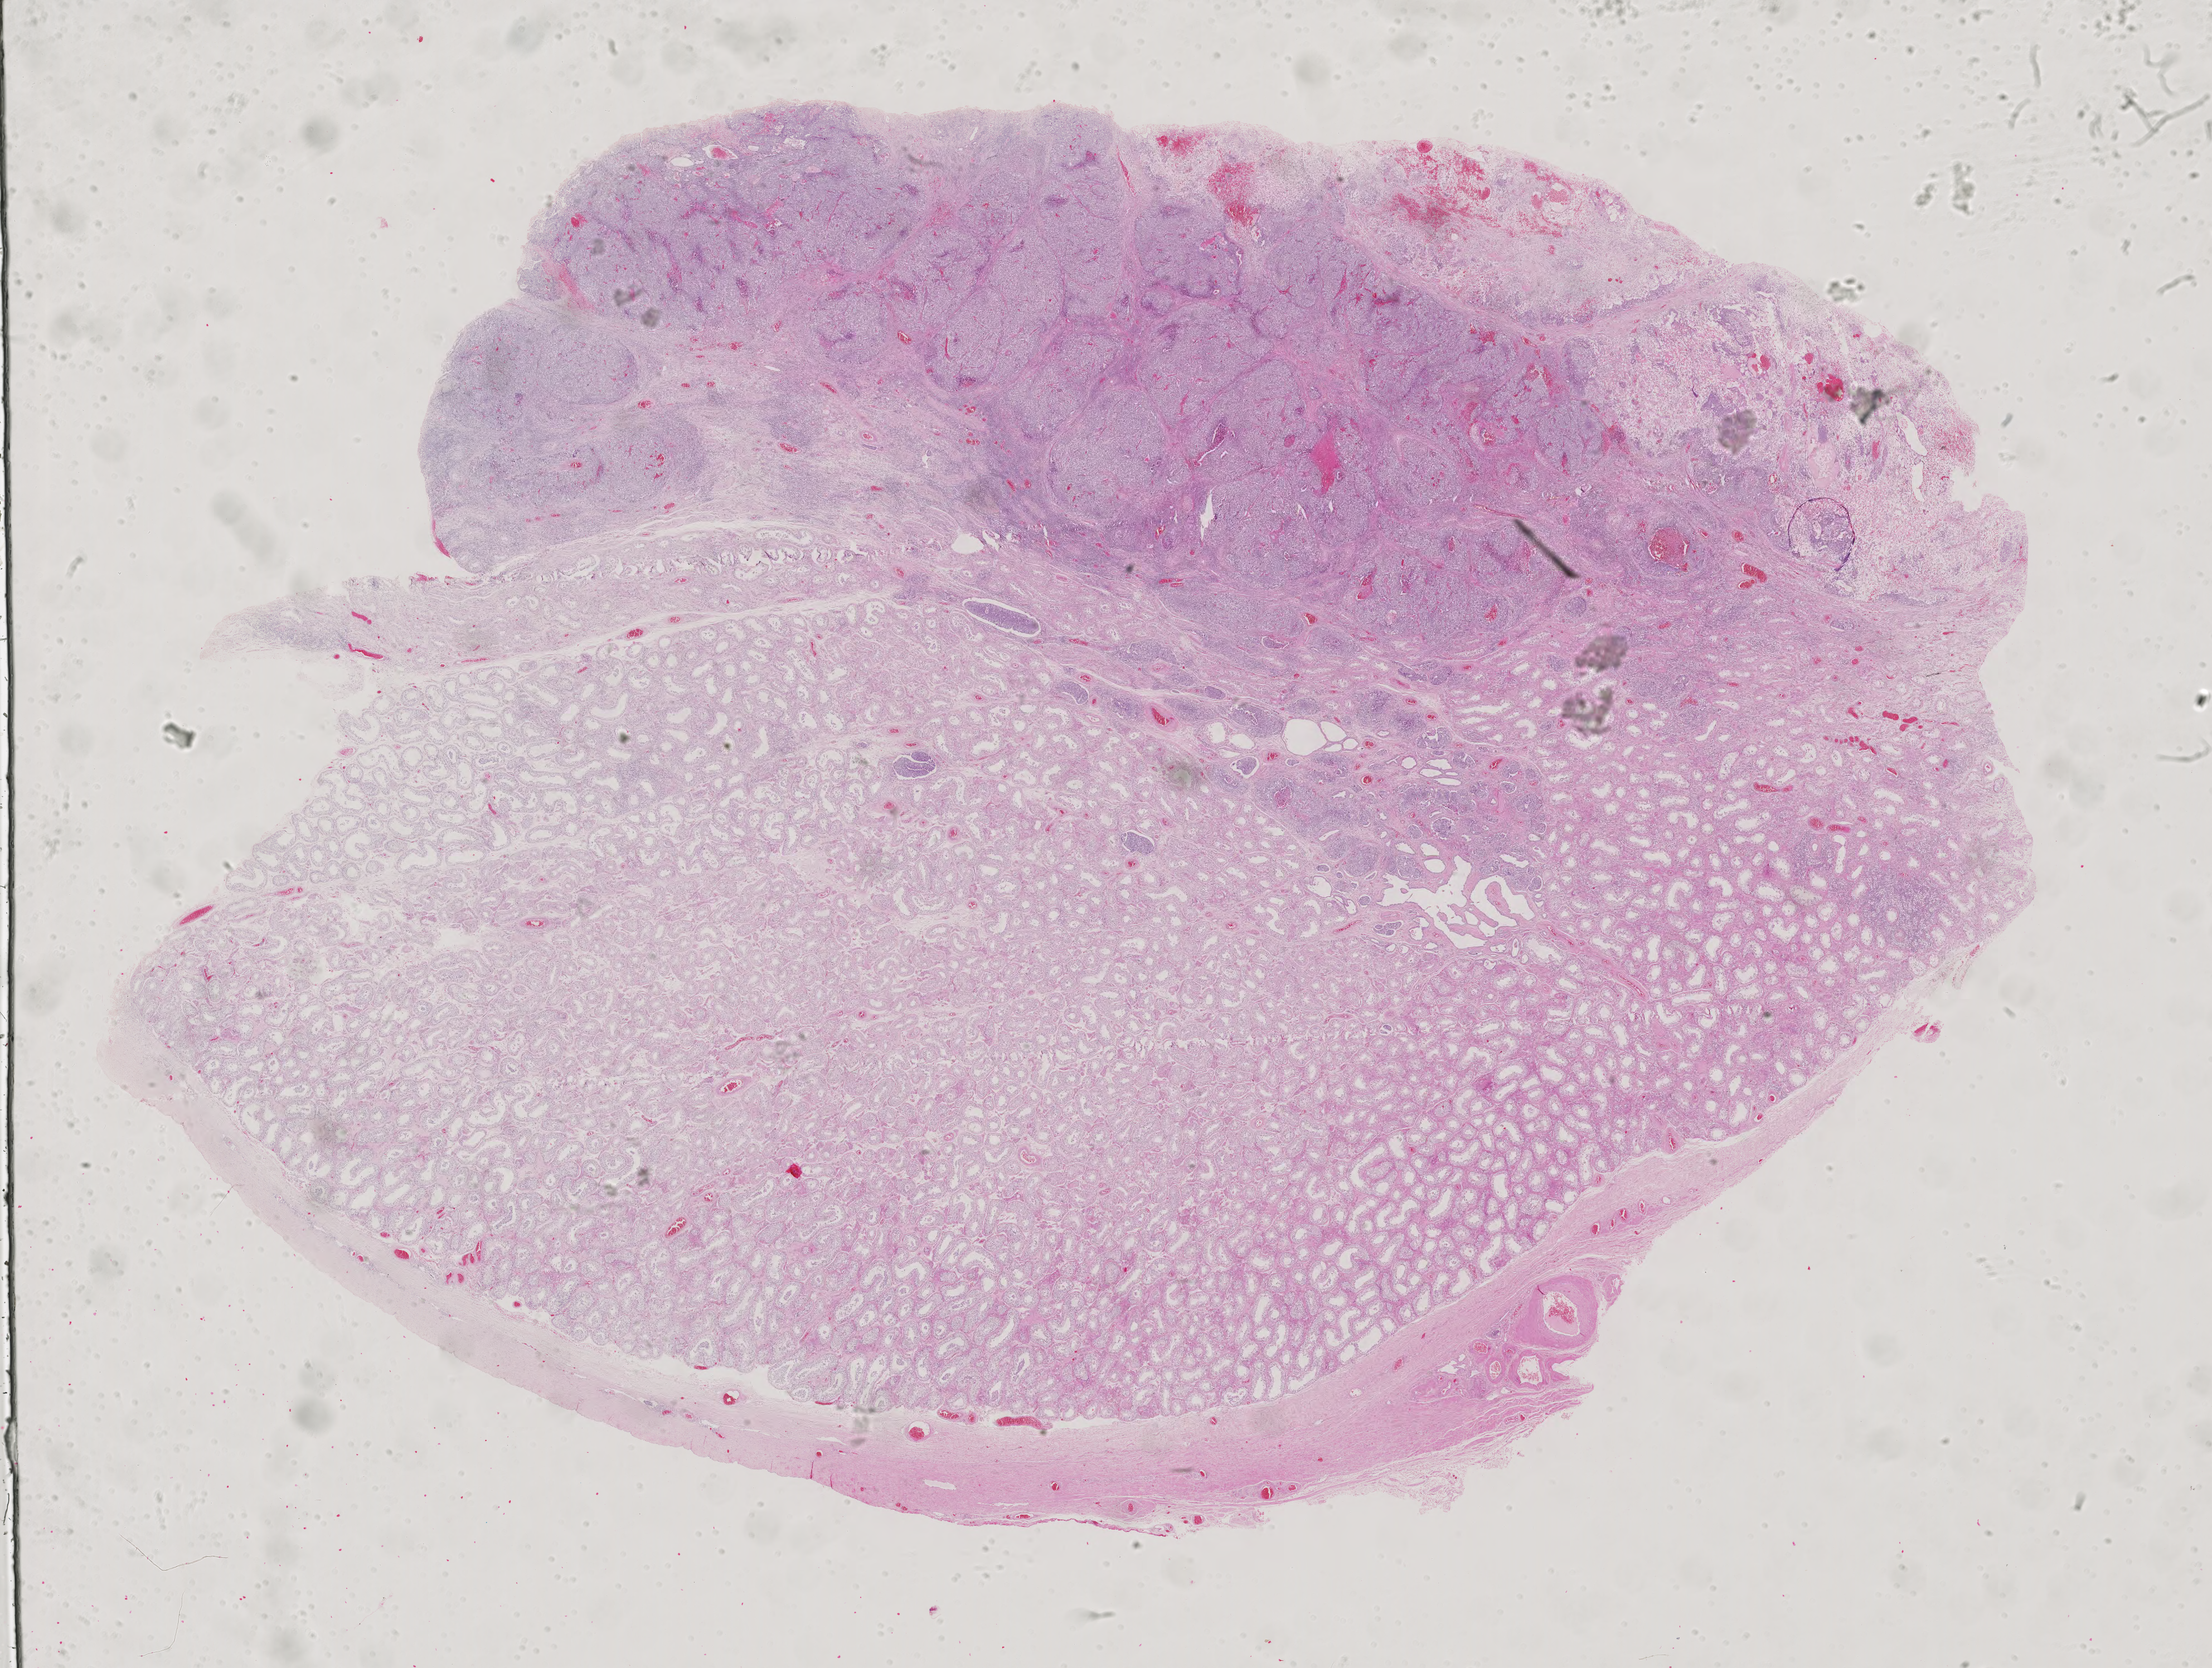
Whole-slide histology image, H&E — low-resolution overview of the scanned area, about 28.9 x 21.8 mm. FFPE section. Sample: primary tumour, testis. Patient: male, age at initial diagnosis 41 years.
- laterality: left
- AJCC pathologic stage: IIIB (6th edition)
- histologic diagnosis: Embryonal carcinoma, NOS